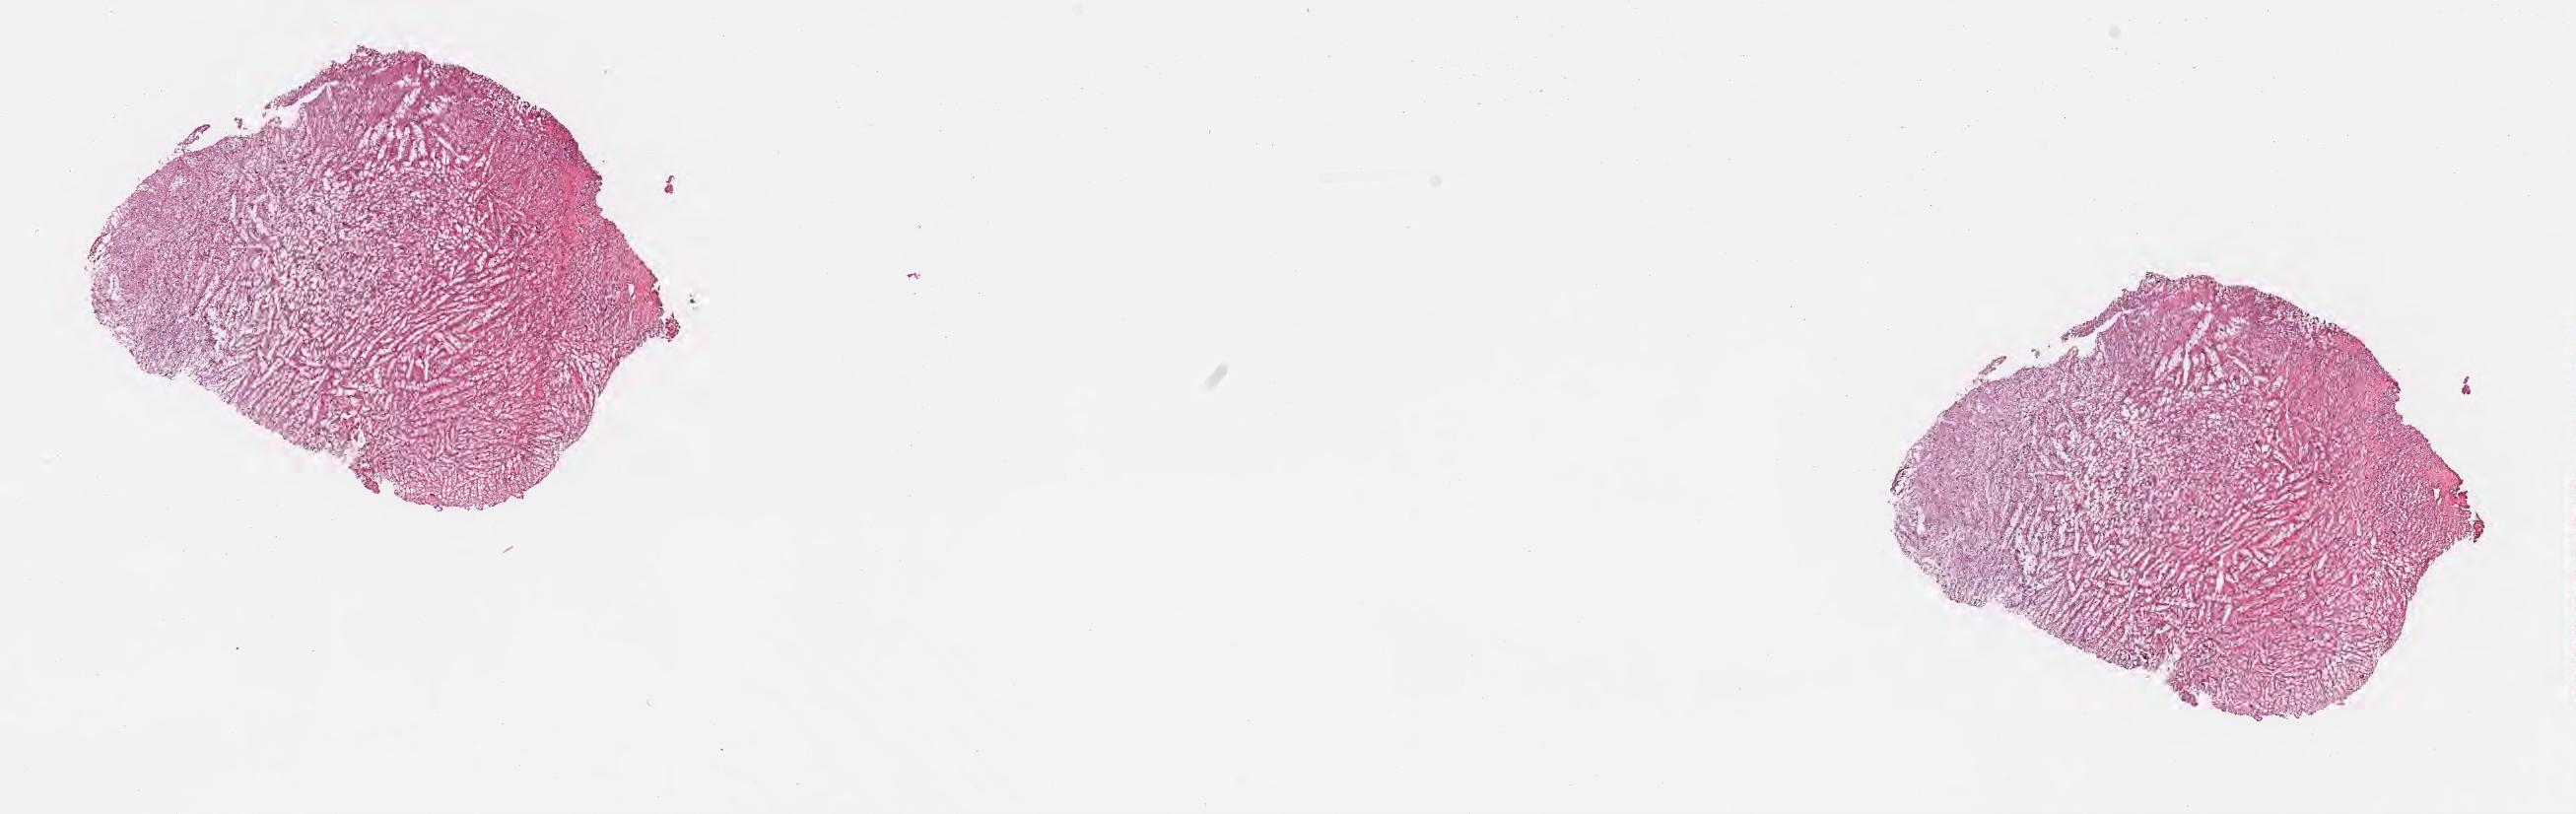
Digitized hematoxylin and eosin (H&E)-stained section — a low-resolution overview of the entire scanned area, about 21.1 x 6.7 mm. Frozen section (tissue freezing medium). Specimen: primary tumor. Site: brain. Male patient; age at initial diagnosis 69 years. Slide review estimates, as recorded: tumor cells 17%, tumor nuclei 53%, stromal cells 68%, necrosis 0%, normal cells 15%. Infiltration values recorded for this section: lymphocyte infiltration 0%, monocyte infiltration 0%, neutrophil infiltration 0%.
- section: top of the tissue portion
- diagnosis: Glioblastoma, NOS